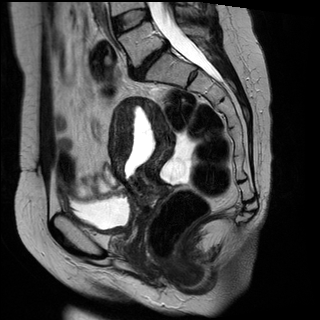
Pelvic MRI for cervical cancer, one sagittal slice; slice 16 of 29 in the series (ordered by position); T2-weighted; 1.5 T; TE 89 ms, TR 2930 ms; 4 mm slice thickness; 320 × 320 image matrix, field of view 260 × 260 mm. Patient: female, 45 years.
Outlined on this slice (outlined manually by an expert reader):
- uterus and cervix: bounding box <109,97,175,220> (left, top, right, bottom; pixels)